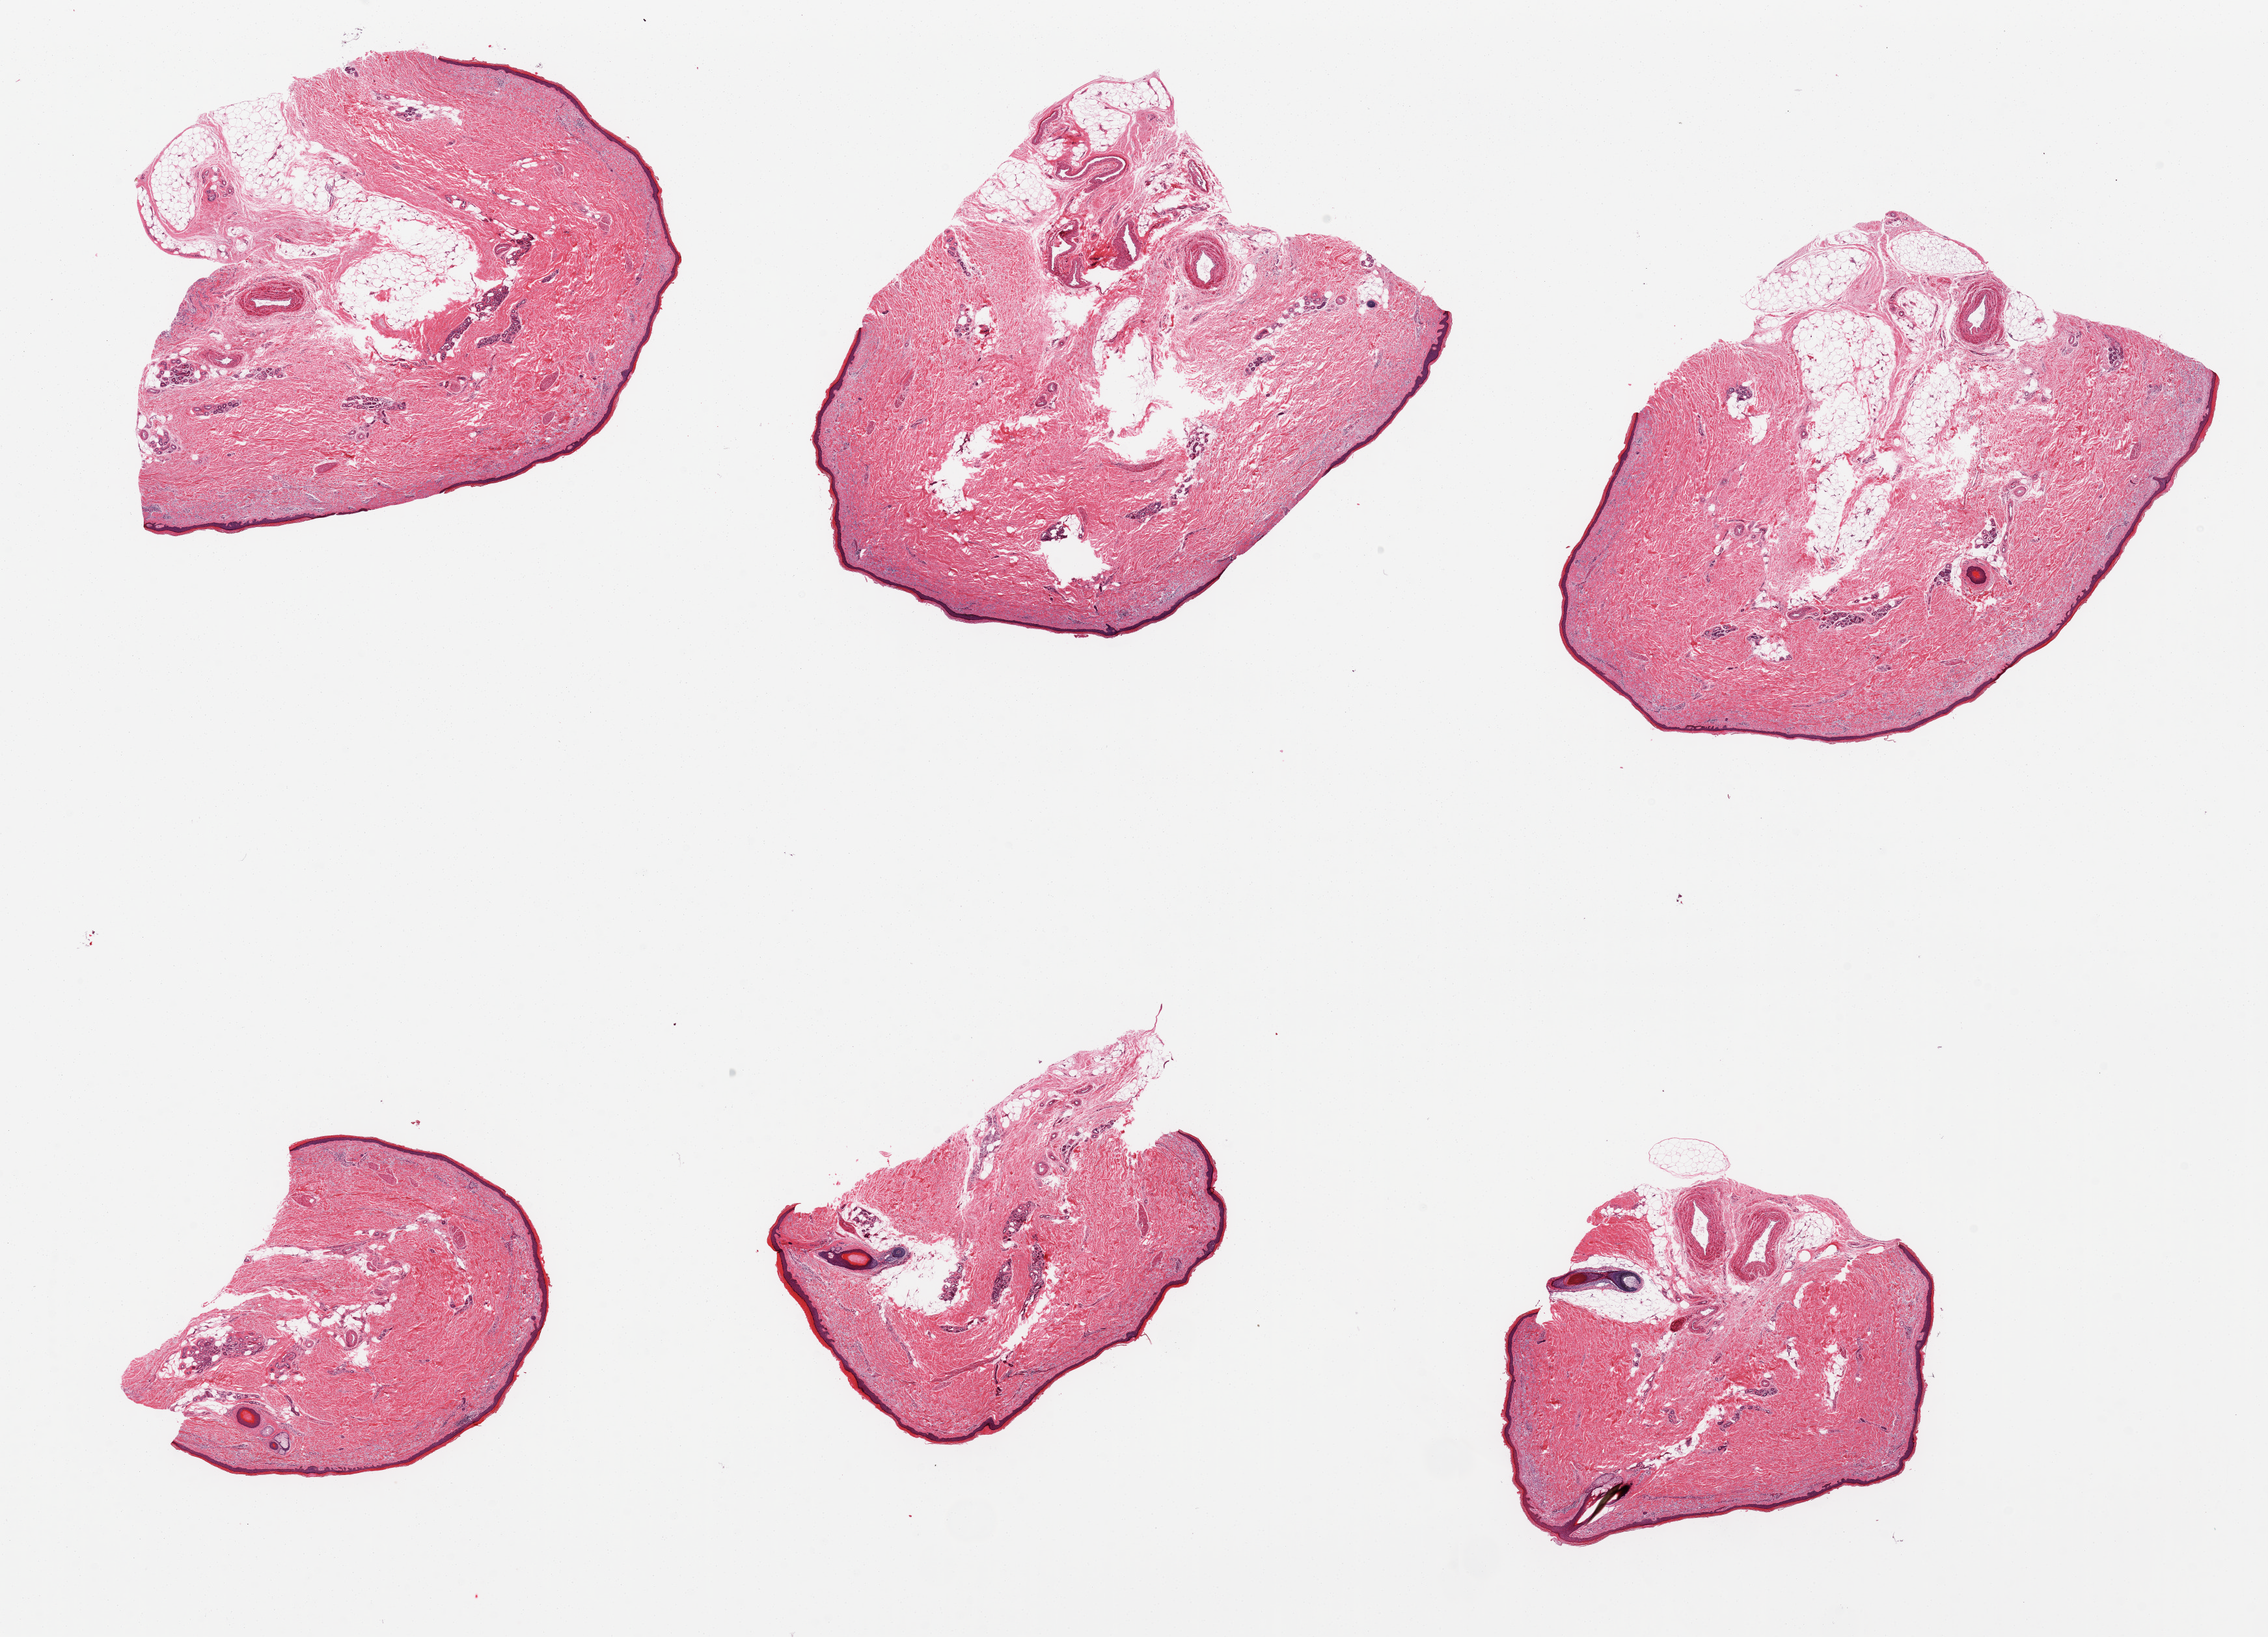
Digitized H&E-stained section — shown as a low-resolution overview of the whole scanned area (about 27.6 x 19.9 mm, from a 20x scan), PAXgene-fixed paraffin-embedded (PFPE) section, target tissue: skin of lower leg, donor tissue sample. Donor sex: male.
- reviewer comment on this tissue sample: 6 pieces, include 5-10% attached and internal adipose tissue, squamous epithelium is 30-42 microns thick